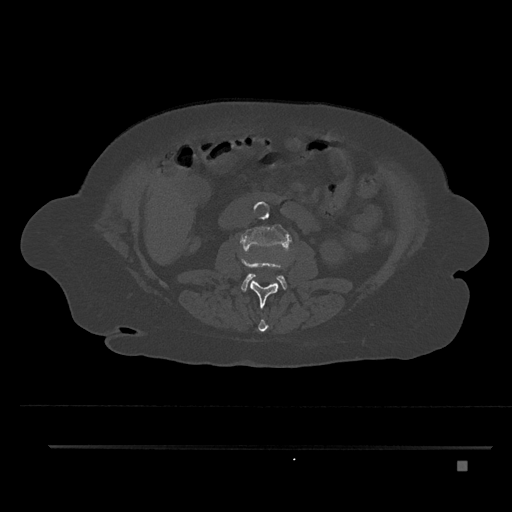
CT including the spine, one axial slice. Position 162 of 797 along the scan axis. Reconstruction kernel Br40s/3. 120 kVp. Bone window (W 1800 / L 400 HU). 0.5 mm slice thickness. 512 × 512 image matrix, field of view 437 × 437 mm. Female patient, age 76 years. From the clinical record (not read from this slice): primary cancer: lung; vertebrae with lytic lesions (as recorded): T11, L3.
Structures marked on this image (semi-automatic segmentation, software-assisted and operator-edited):
- L1 vertebra: bounding box <258,319,268,332> (left, top, right, bottom; pixels)
- L2 vertebra: <241,257,283,309>
- L3 vertebra: <241,224,292,292>